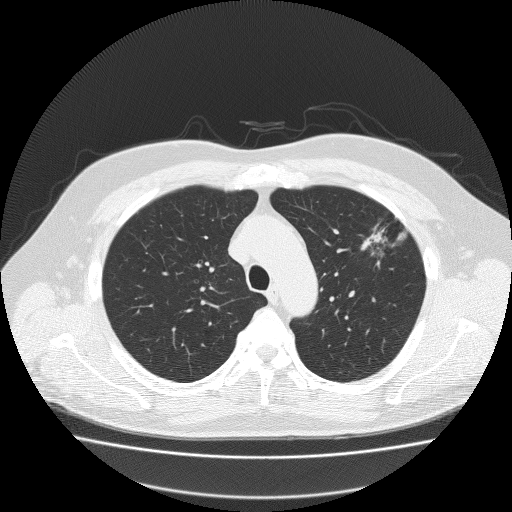
Low-dose screening chest CT, one axial slice; 120 kVp; lung window (W 1500 / L -600 HU); 2 mm slice thickness; 512 × 512 image matrix, field of view 410 × 410 mm.
Annotated regions visible in this slice (outlined manually by an expert reader):
- lesion 1 (tumor, upper lobe of left lung): box from (x=361, y=217) to (x=400, y=259) px